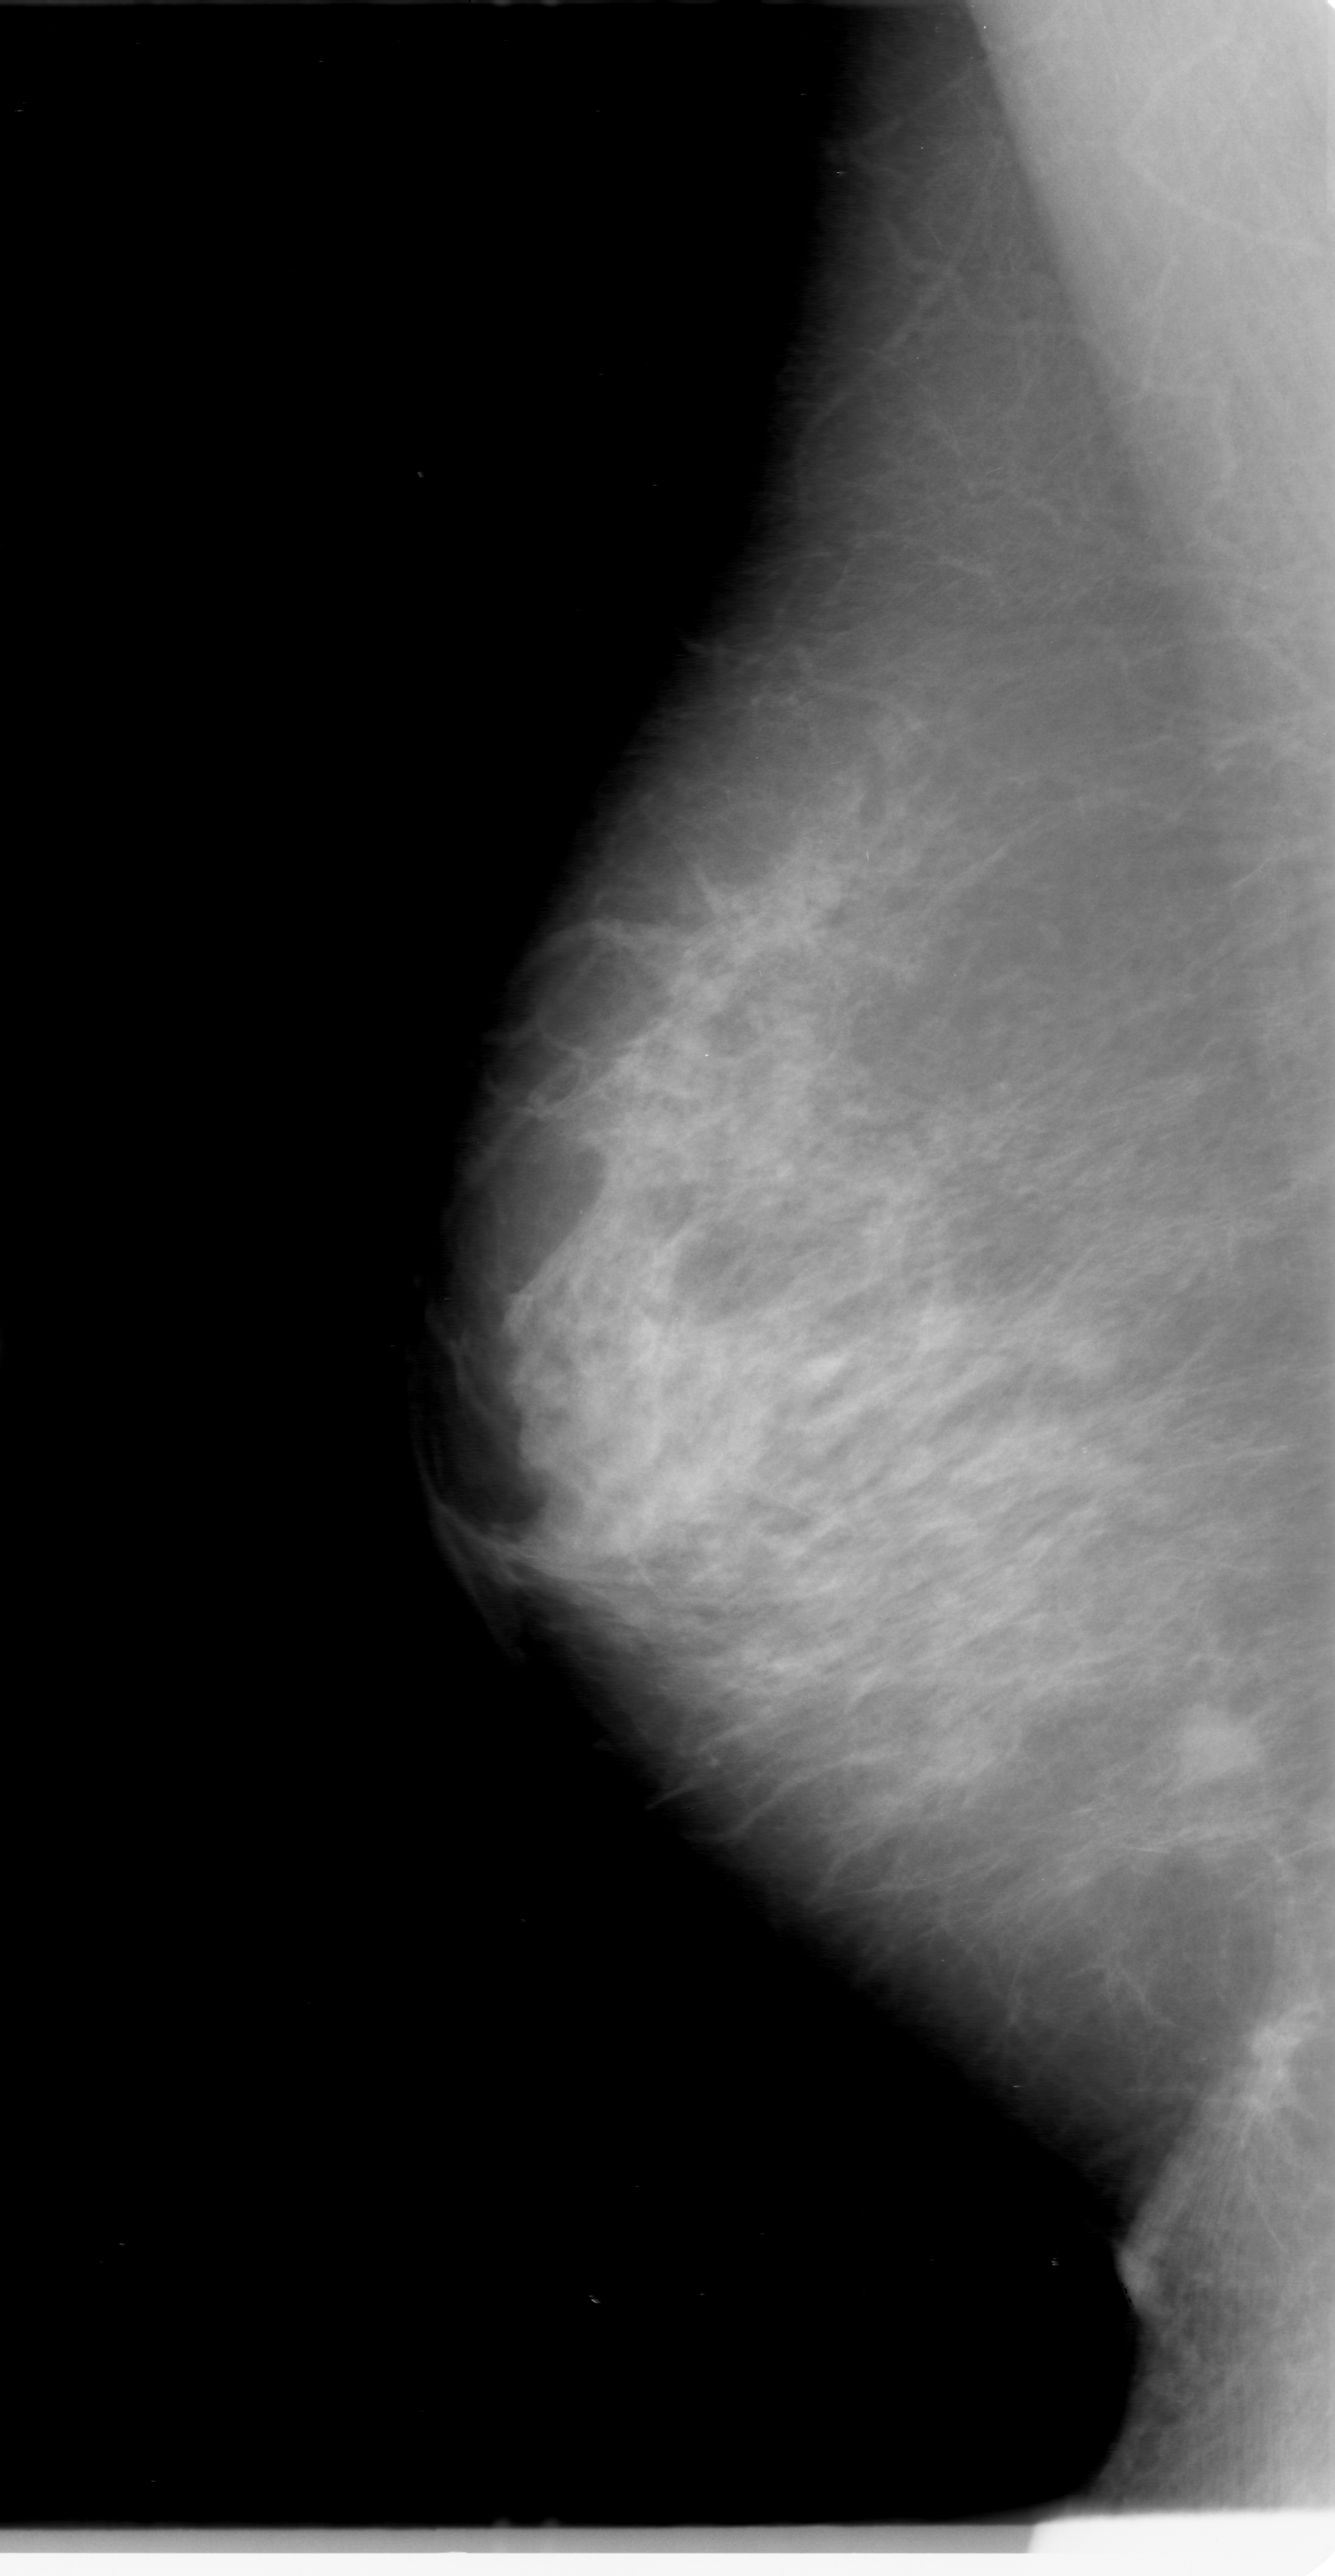
Mammogram (digitized film). Right breast. Mediolateral oblique (MLO) view. Breast composition: scattered fibroglandular densities (BI-RADS density category 2 of 4). 1335 × 2576 image matrix.
Expert-marked regions of interest on this image (one box per marked abnormality):
- mass, shape oval, margins obscured; BI-RADS assessment category 0 (incomplete: needs additional imaging); pathology result (as recorded, not read from the image): malignant: bounding box <1135,1678,1276,1805> (left, top, right, bottom; pixels)